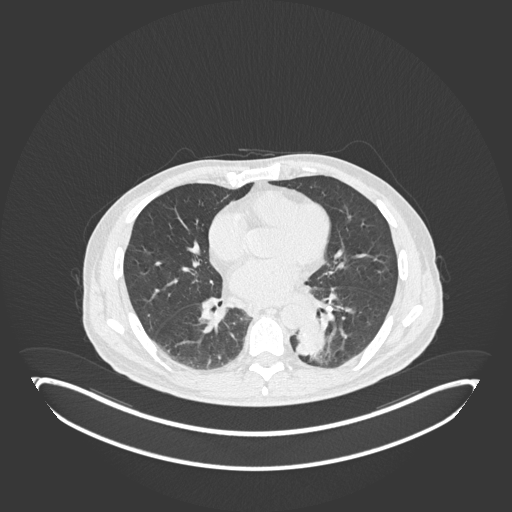
Chest CT, one axial slice; slice 79 of 251 in the series (ordered by position); 120 kVp; lung window (W 1500 / L -600 HU); 1 mm slice thickness; 512 × 512 image matrix. Male patient, age 72 years. Case-level facts recorded for this patient, not image findings: clinical TNM (as recorded): T2b N0 M1.
Structures marked on this image (rectangle marked by the reading radiologist):
- lung tumour (recorded histology: adenocarcinoma): bounding box <292,315,329,358> (left, top, right, bottom; pixels)